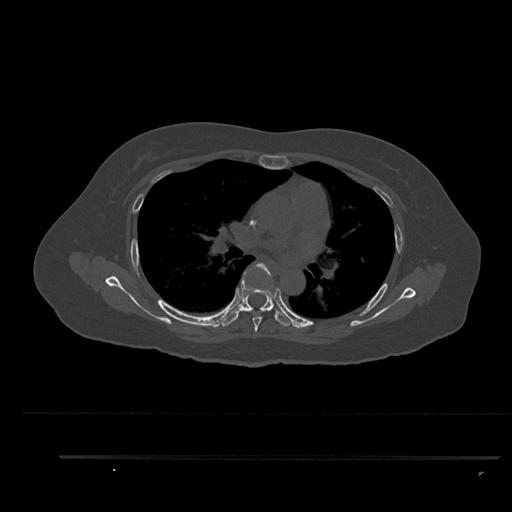
CT including the spine, one axial slice; position 577 of 797 along the scan axis; reconstruction kernel Br40s/3; 120 kVp; bone window (W 1800 / L 400 HU); 0.5 mm slice thickness; 512 × 512 image matrix, field of view 408 × 408 mm. Patient: female, 44 years. From the clinical record (not read from this slice): primary cancer: renal; vertebrae with lytic lesions (as recorded): L1.
Structures marked on this image (semi-automatic segmentation, software-assisted and operator-edited):
- T5 vertebra: bounding box (x1, y1, x2, y2) in pixels: (249, 263, 272, 332)
- T6 vertebra: (221, 279, 292, 327)